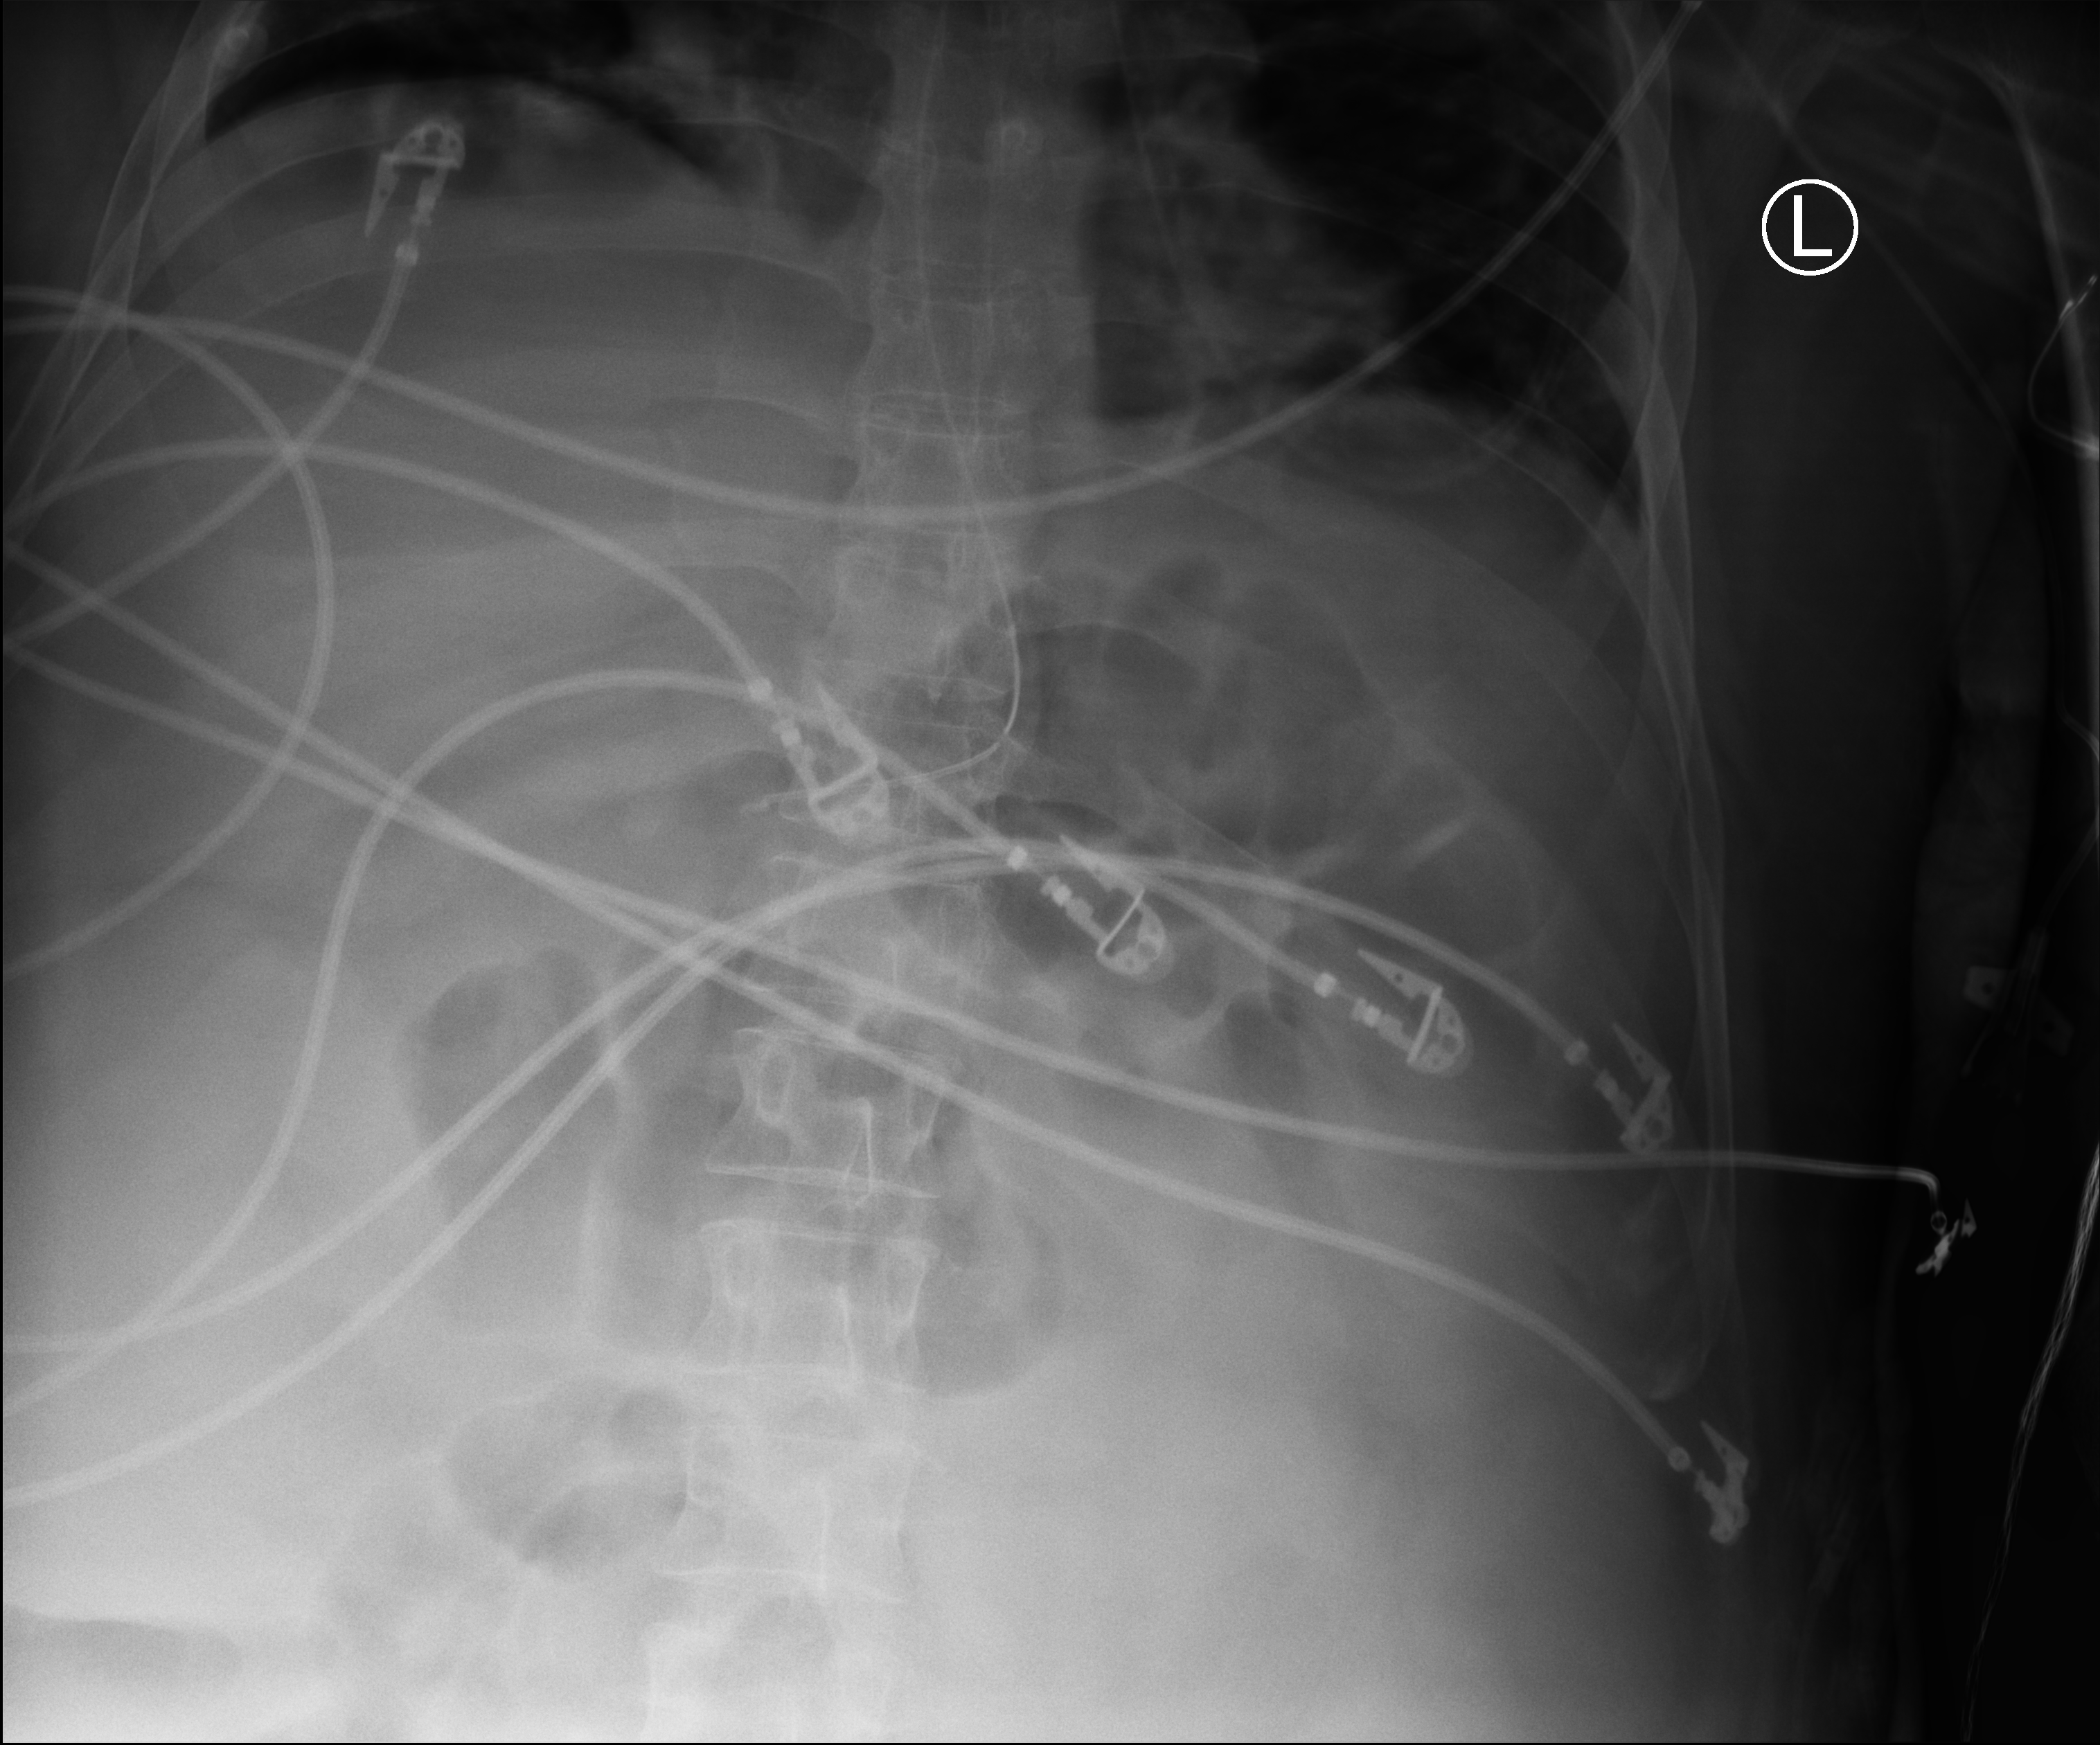
Bedside abdomen radiograph (computed radiography), anteroposterior (AP) projection. Adult patient hospitalised with COVID-19, age 18–59 years.
Admission-level facts for this patient (not findings on this image; timing relative to this image not recorded): mechanically ventilated during this hospital stay: yes; admitted to intensive care during this hospital stay: yes.